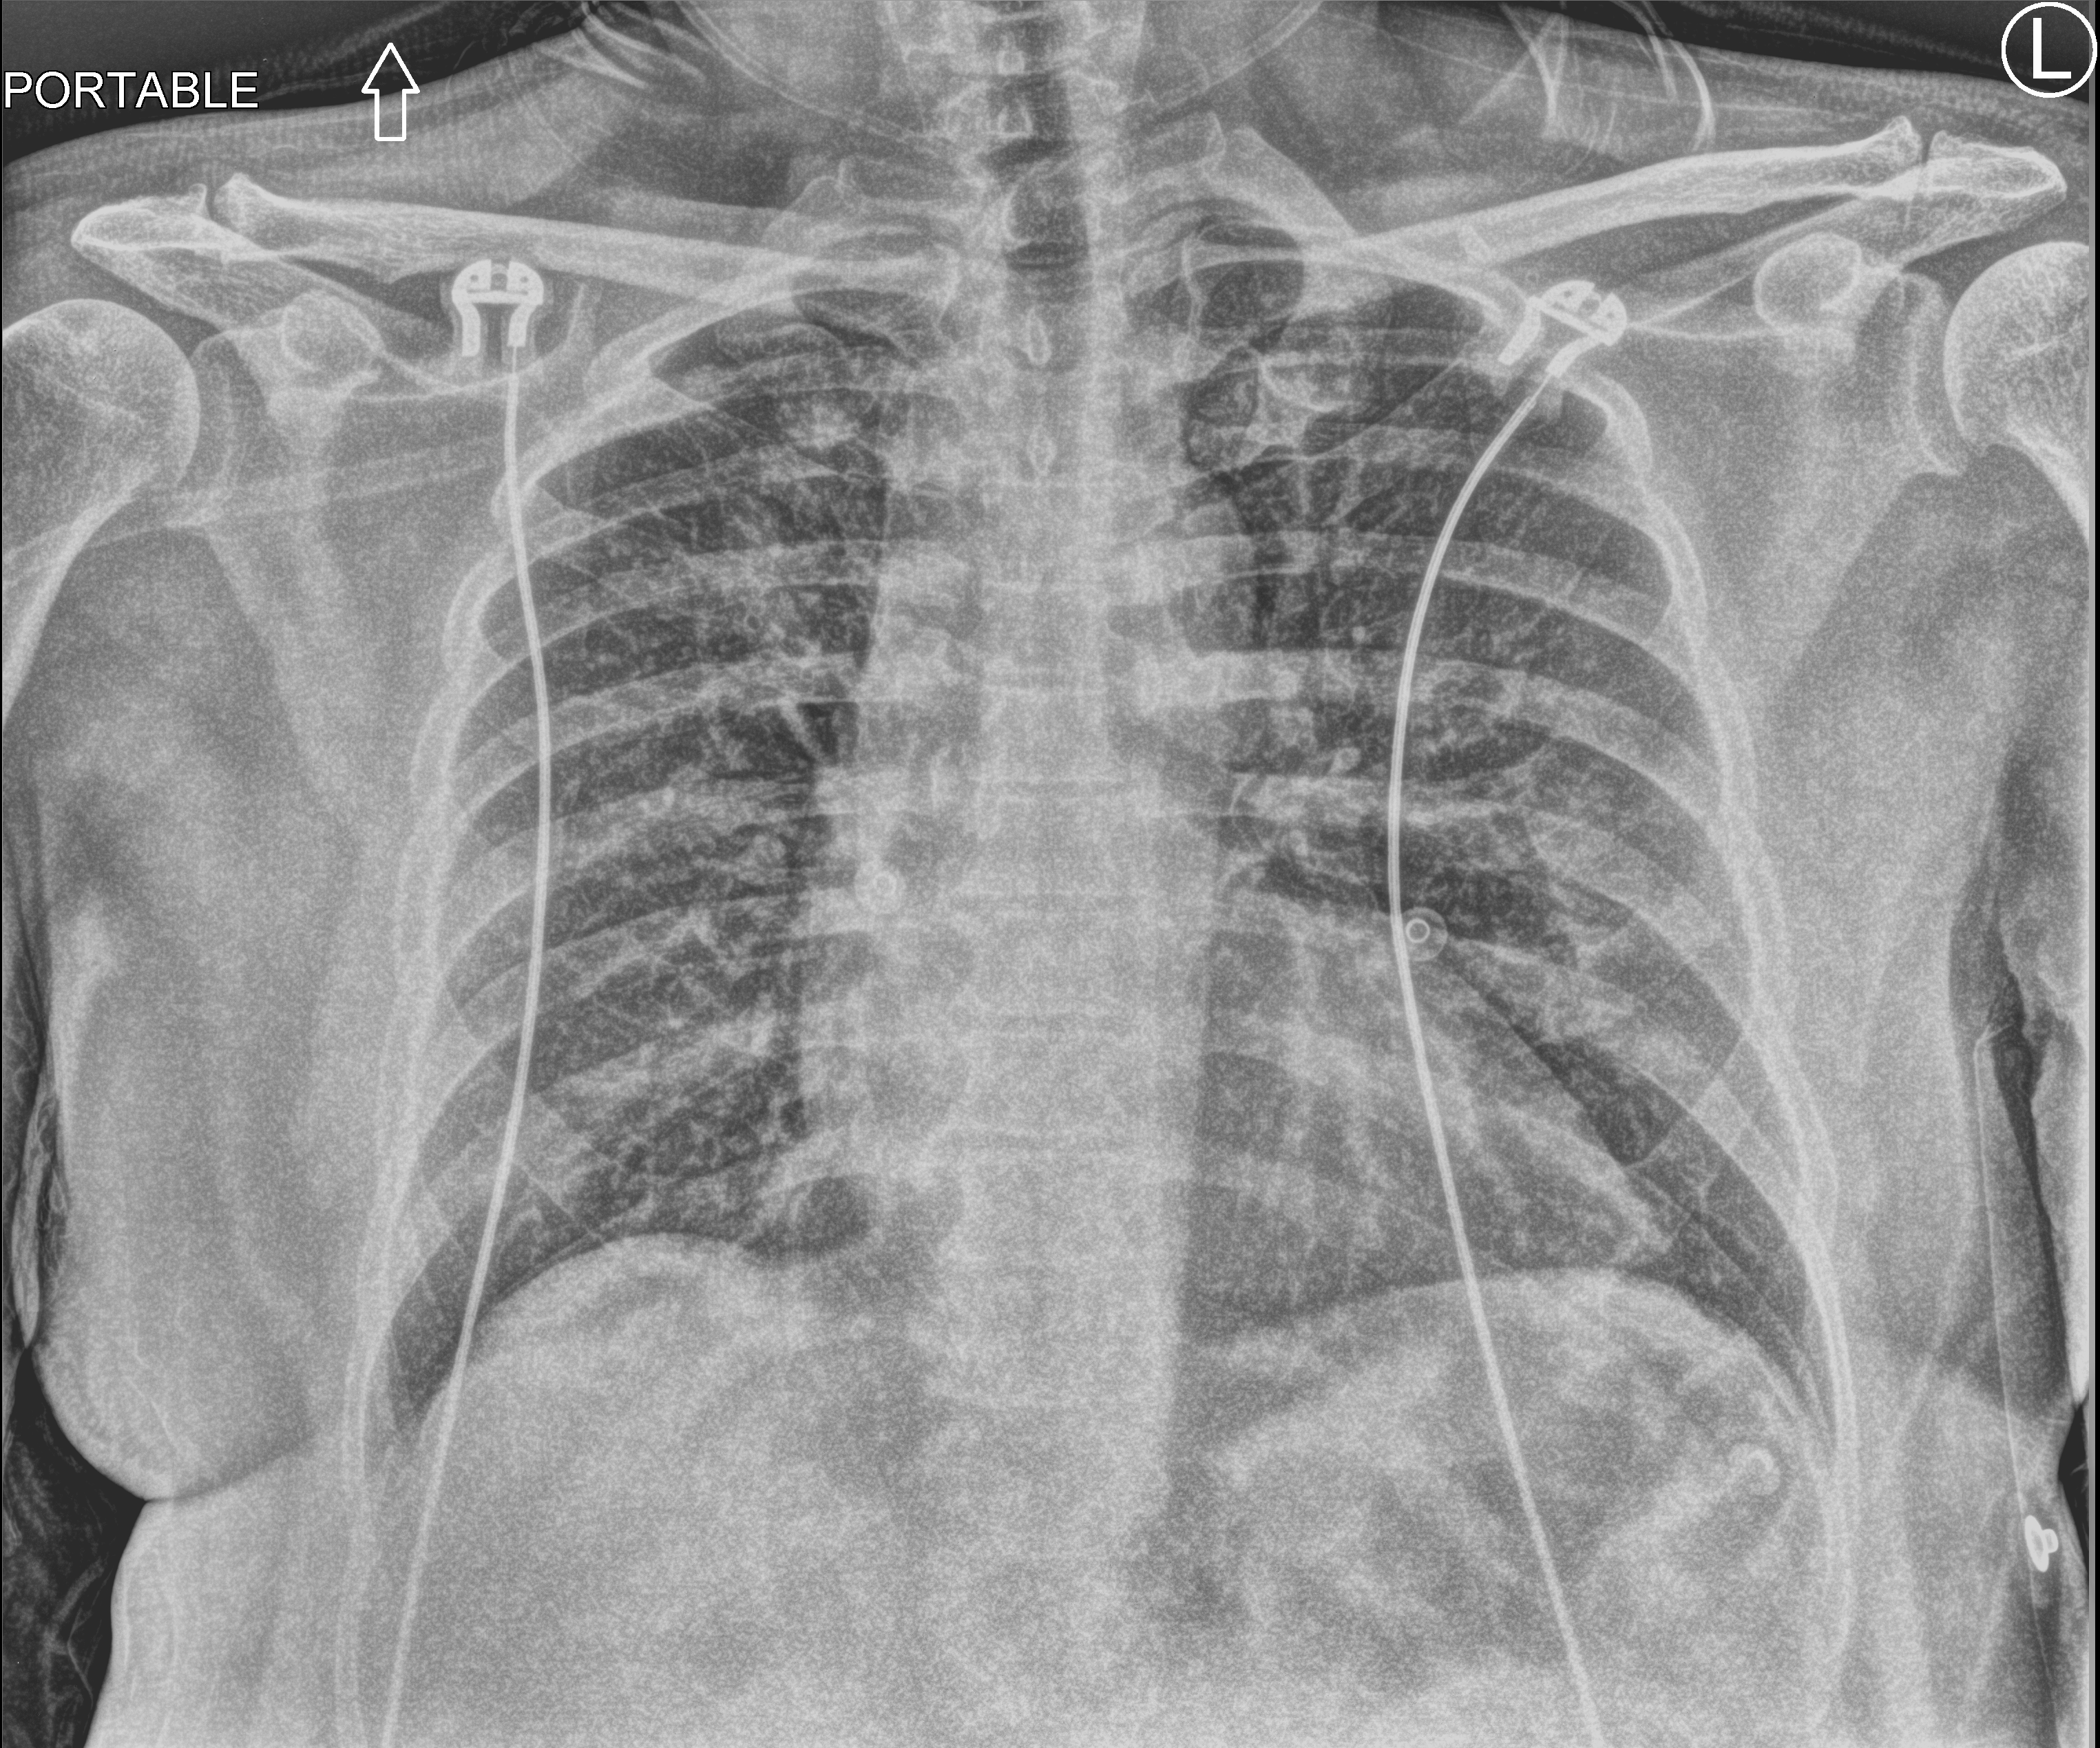
Portable chest radiograph. Patient hospitalised with COVID-19; male, aged 18–59 years.
Admission-level facts for this patient (not findings on this image; timing relative to this image not recorded): smoking status (admission record): never.